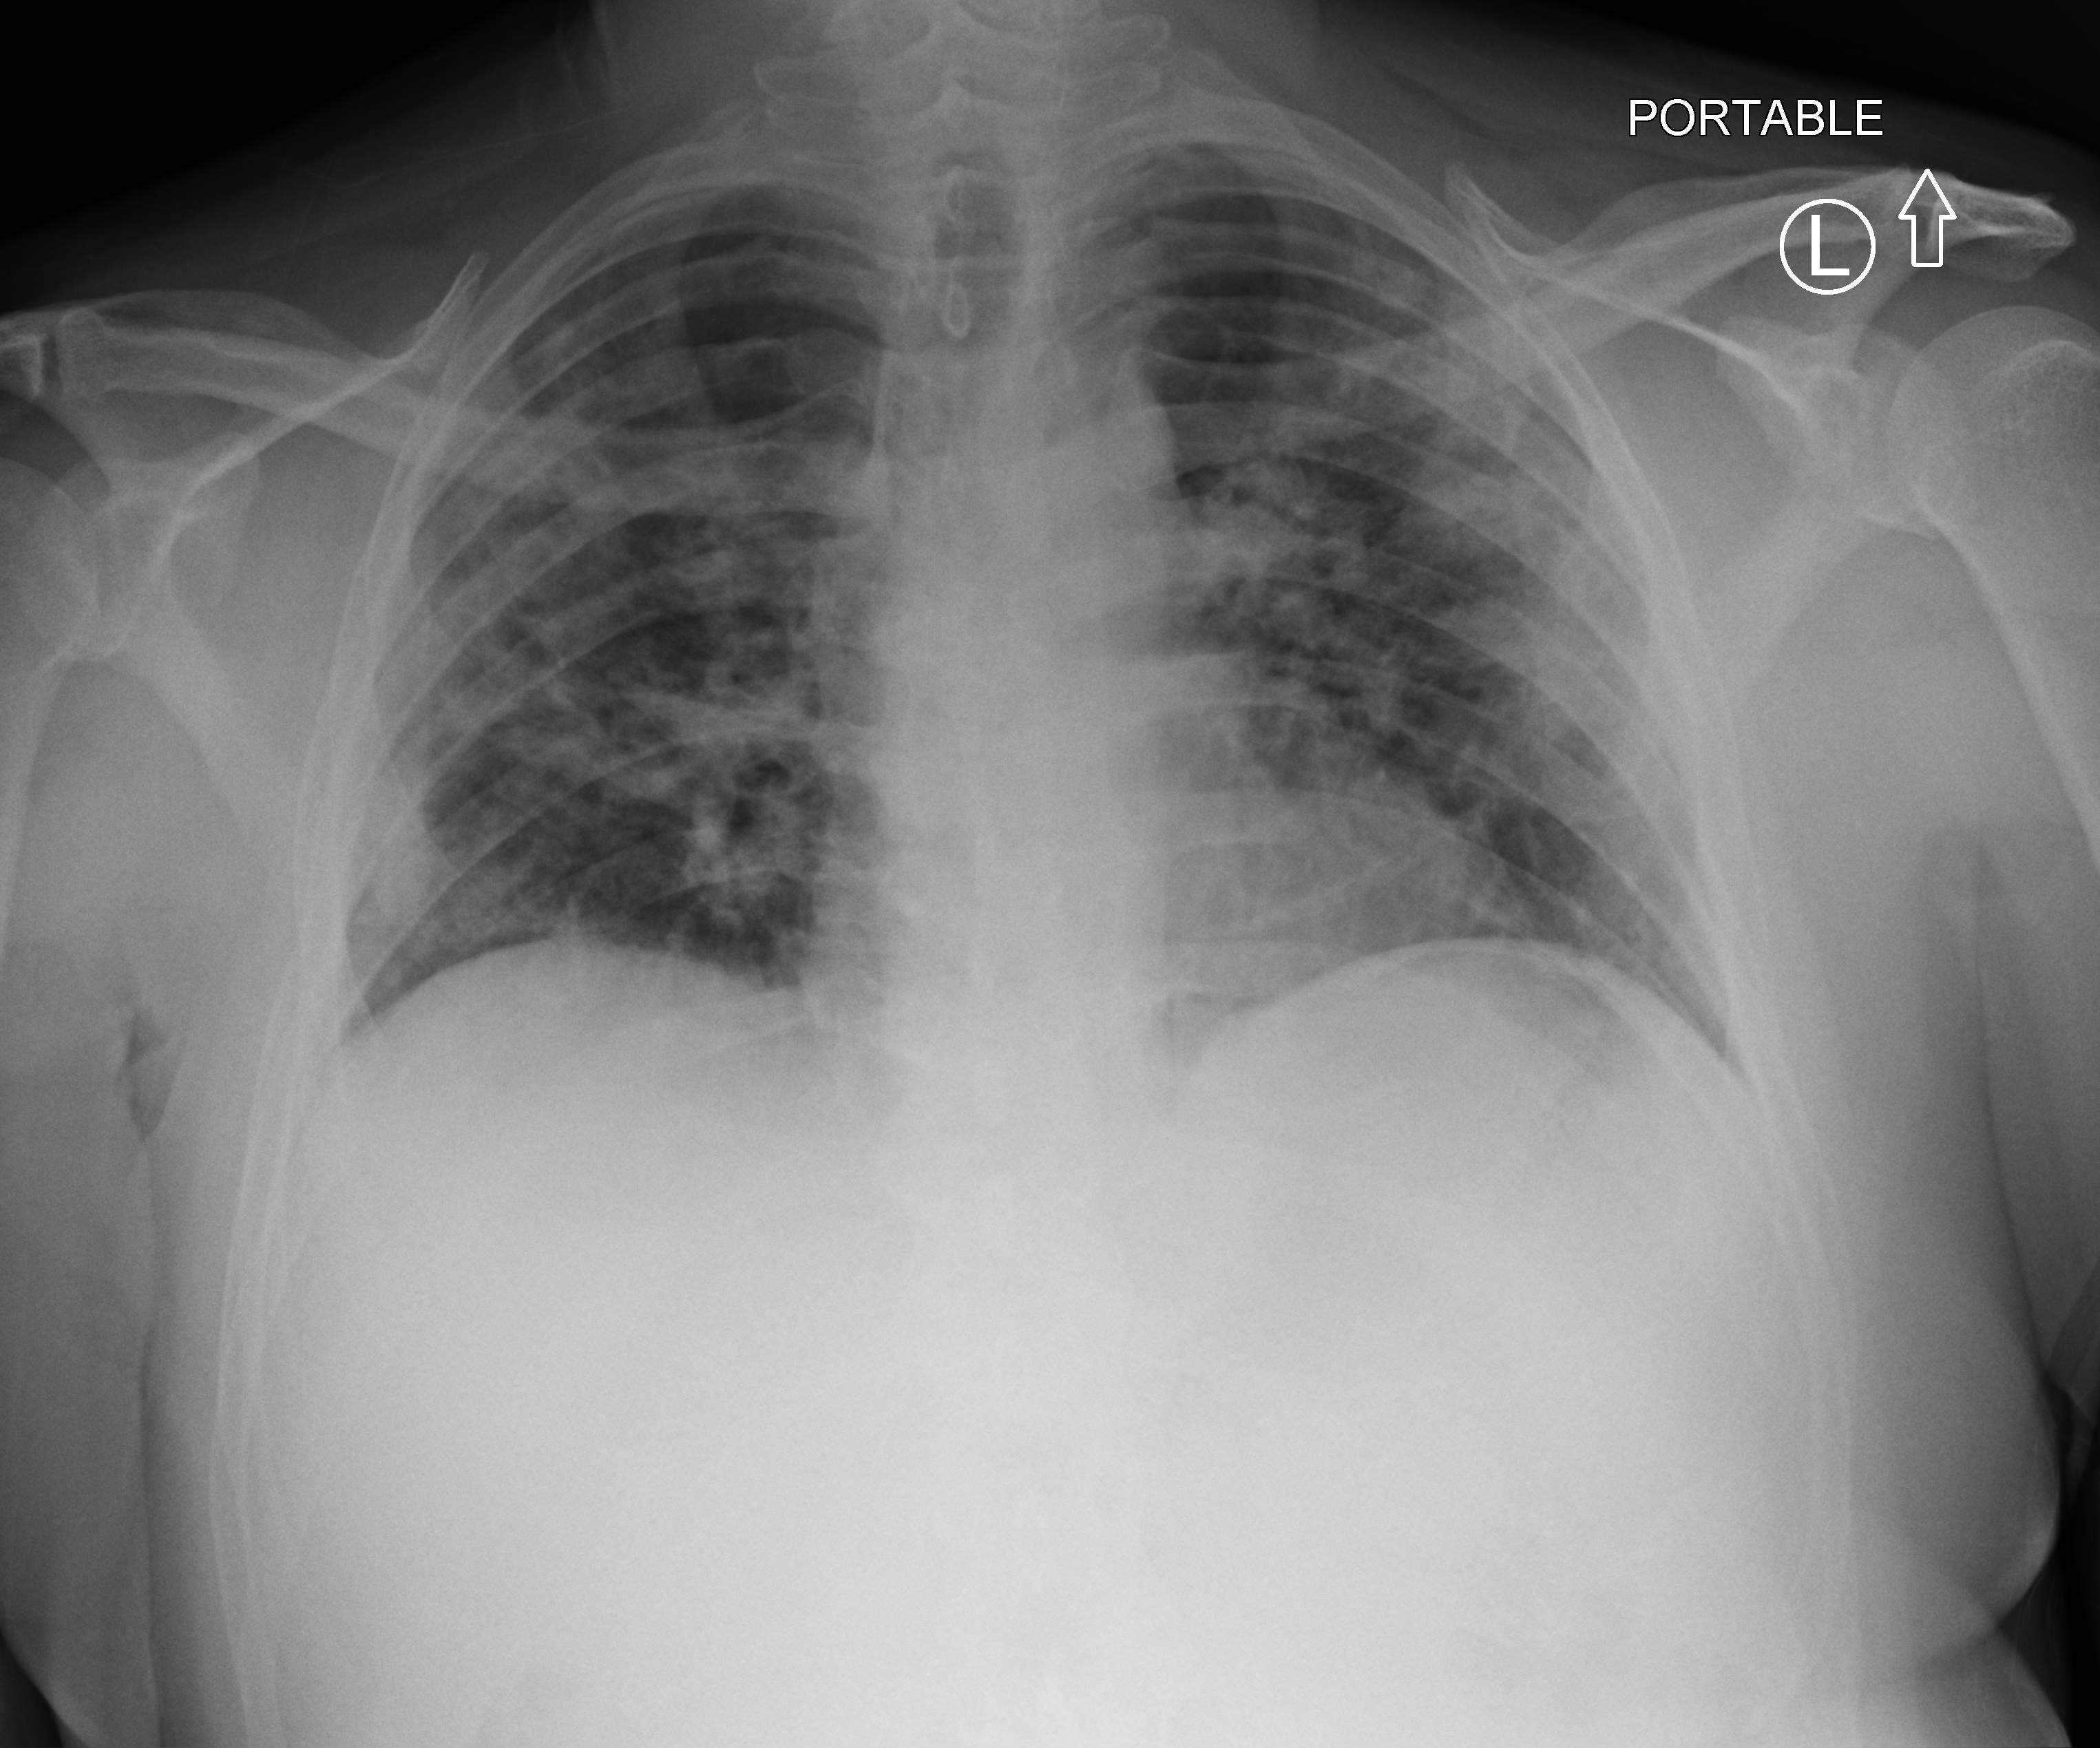
Bedside chest radiograph (computed radiography); anteroposterior (AP) projection. Male patient hospitalised with COVID-19, age 18–59 years.
Hospital-stay facts (about this admission, not read from this image; timing relative to this image not recorded):
- mechanically ventilated during this hospital stay: no
- hypertension (admission record): no